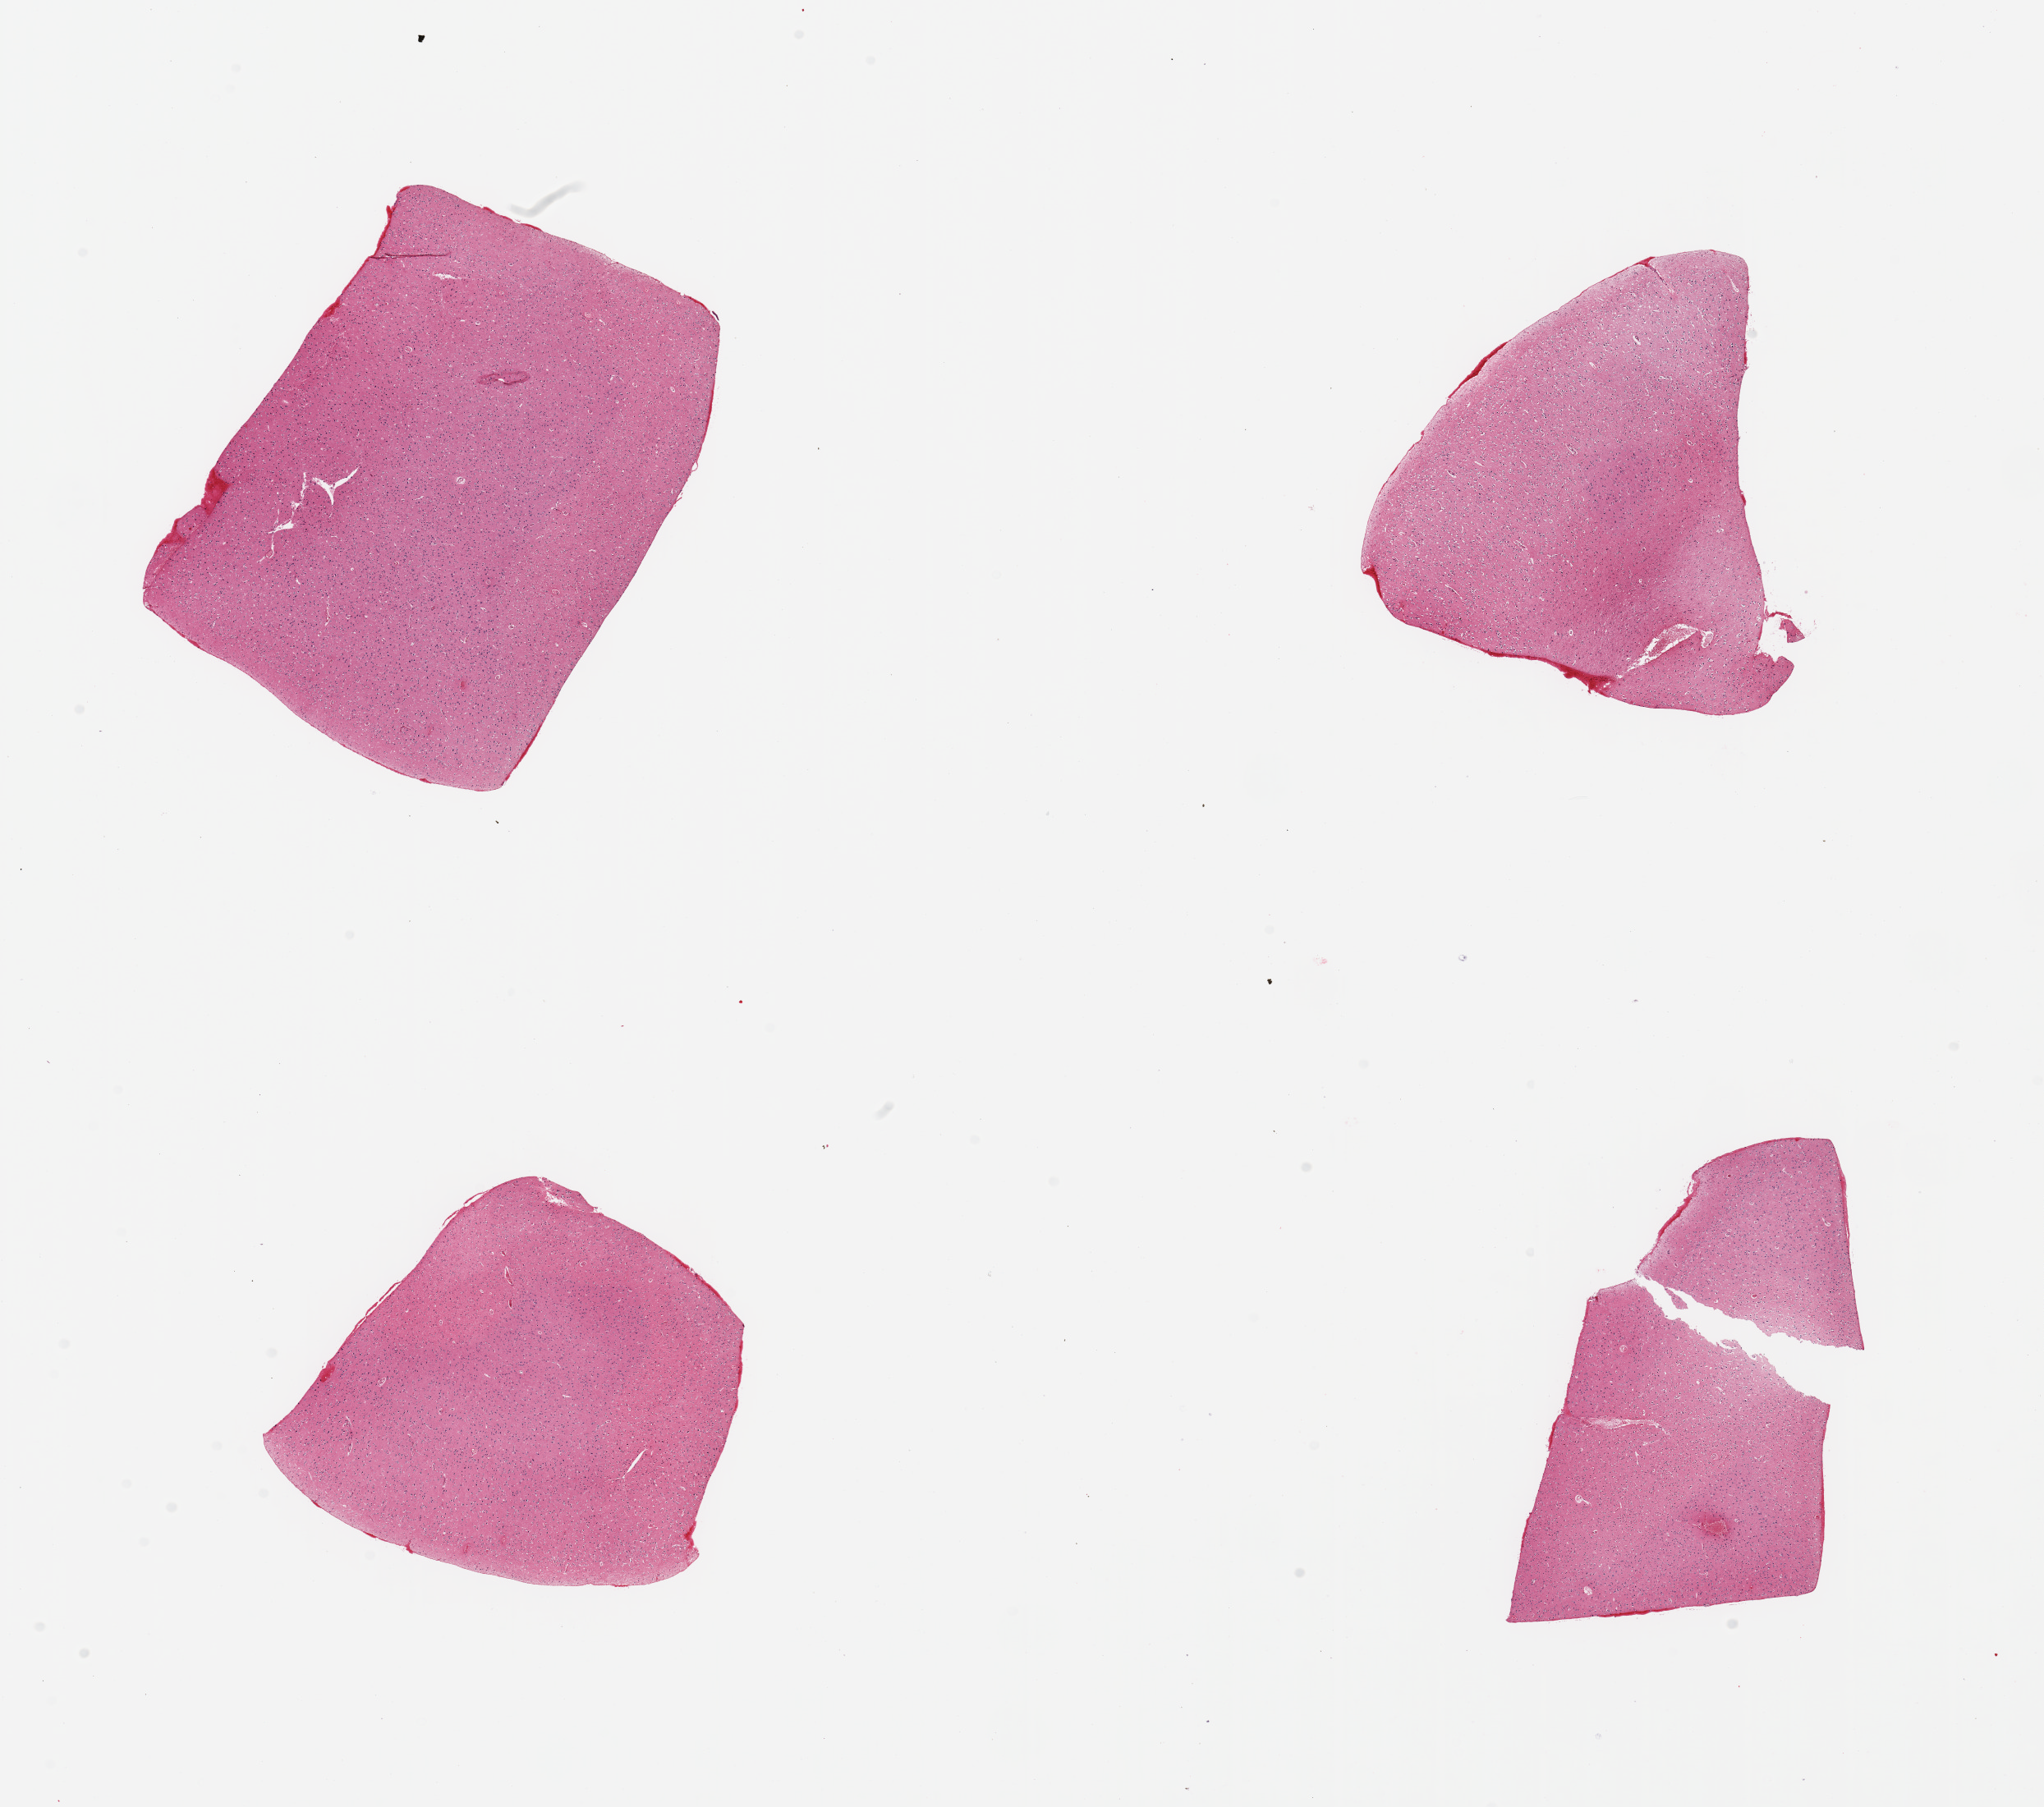
Whole-slide image, hematoxylin and eosin (H&E) stain — low-resolution overview of the scanned area, about 19.7 x 17.4 mm. PAXgene-fixed paraffin-embedded (PFPE) section. Sampled site (target tissue): cerebral cortex. Donor tissue sample. Donor sex: female.
Review note (as recorded): 4 pieces.